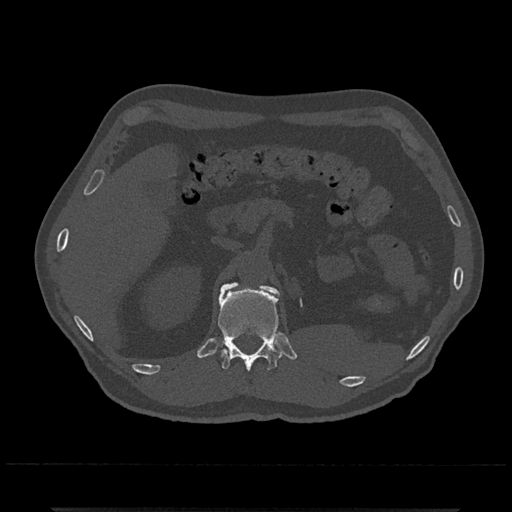
CT including the spine, one axial slice; slice 424 of 797 in the series (ordered by position); reconstruction kernel Br40s/3; 120 kVp; bone window (W 1800 / L 400 HU); 0.5 mm slice thickness; 512 × 512 image matrix, field of view 393 × 393 mm. Male patient, age 67 years. Case-level facts recorded for this patient, not image findings: primary cancer: prostate.
Structures marked on this image (semi-automatic segmentation, software-assisted and operator-edited):
- L1 vertebra: bounding box <258,283,276,294> (left, top, right, bottom; pixels)
- T12 vertebra: <218,283,282,372>